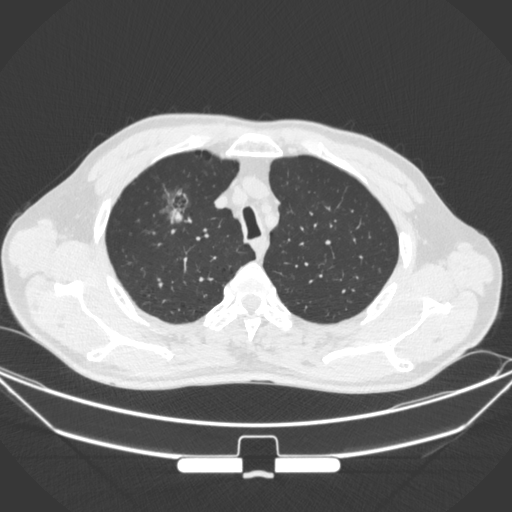
Chest CT, one axial slice; slice 281 of 355 in the series (ordered by position); lung window (W 1500 / L -600 HU); 1 mm slice thickness; 512 × 512 image matrix, field of view 399 × 399 mm. Patient: male, 67 years. From the clinical record (not read from this slice): clinical TNM (as recorded): T1c N0 M0; histopathological grade: G2.
Outlined on this slice (bounding box drawn by a radiologist):
- lung tumour (recorded histology: adenocarcinoma): bounding box (x1, y1, x2, y2) in pixels: (144, 177, 203, 242)